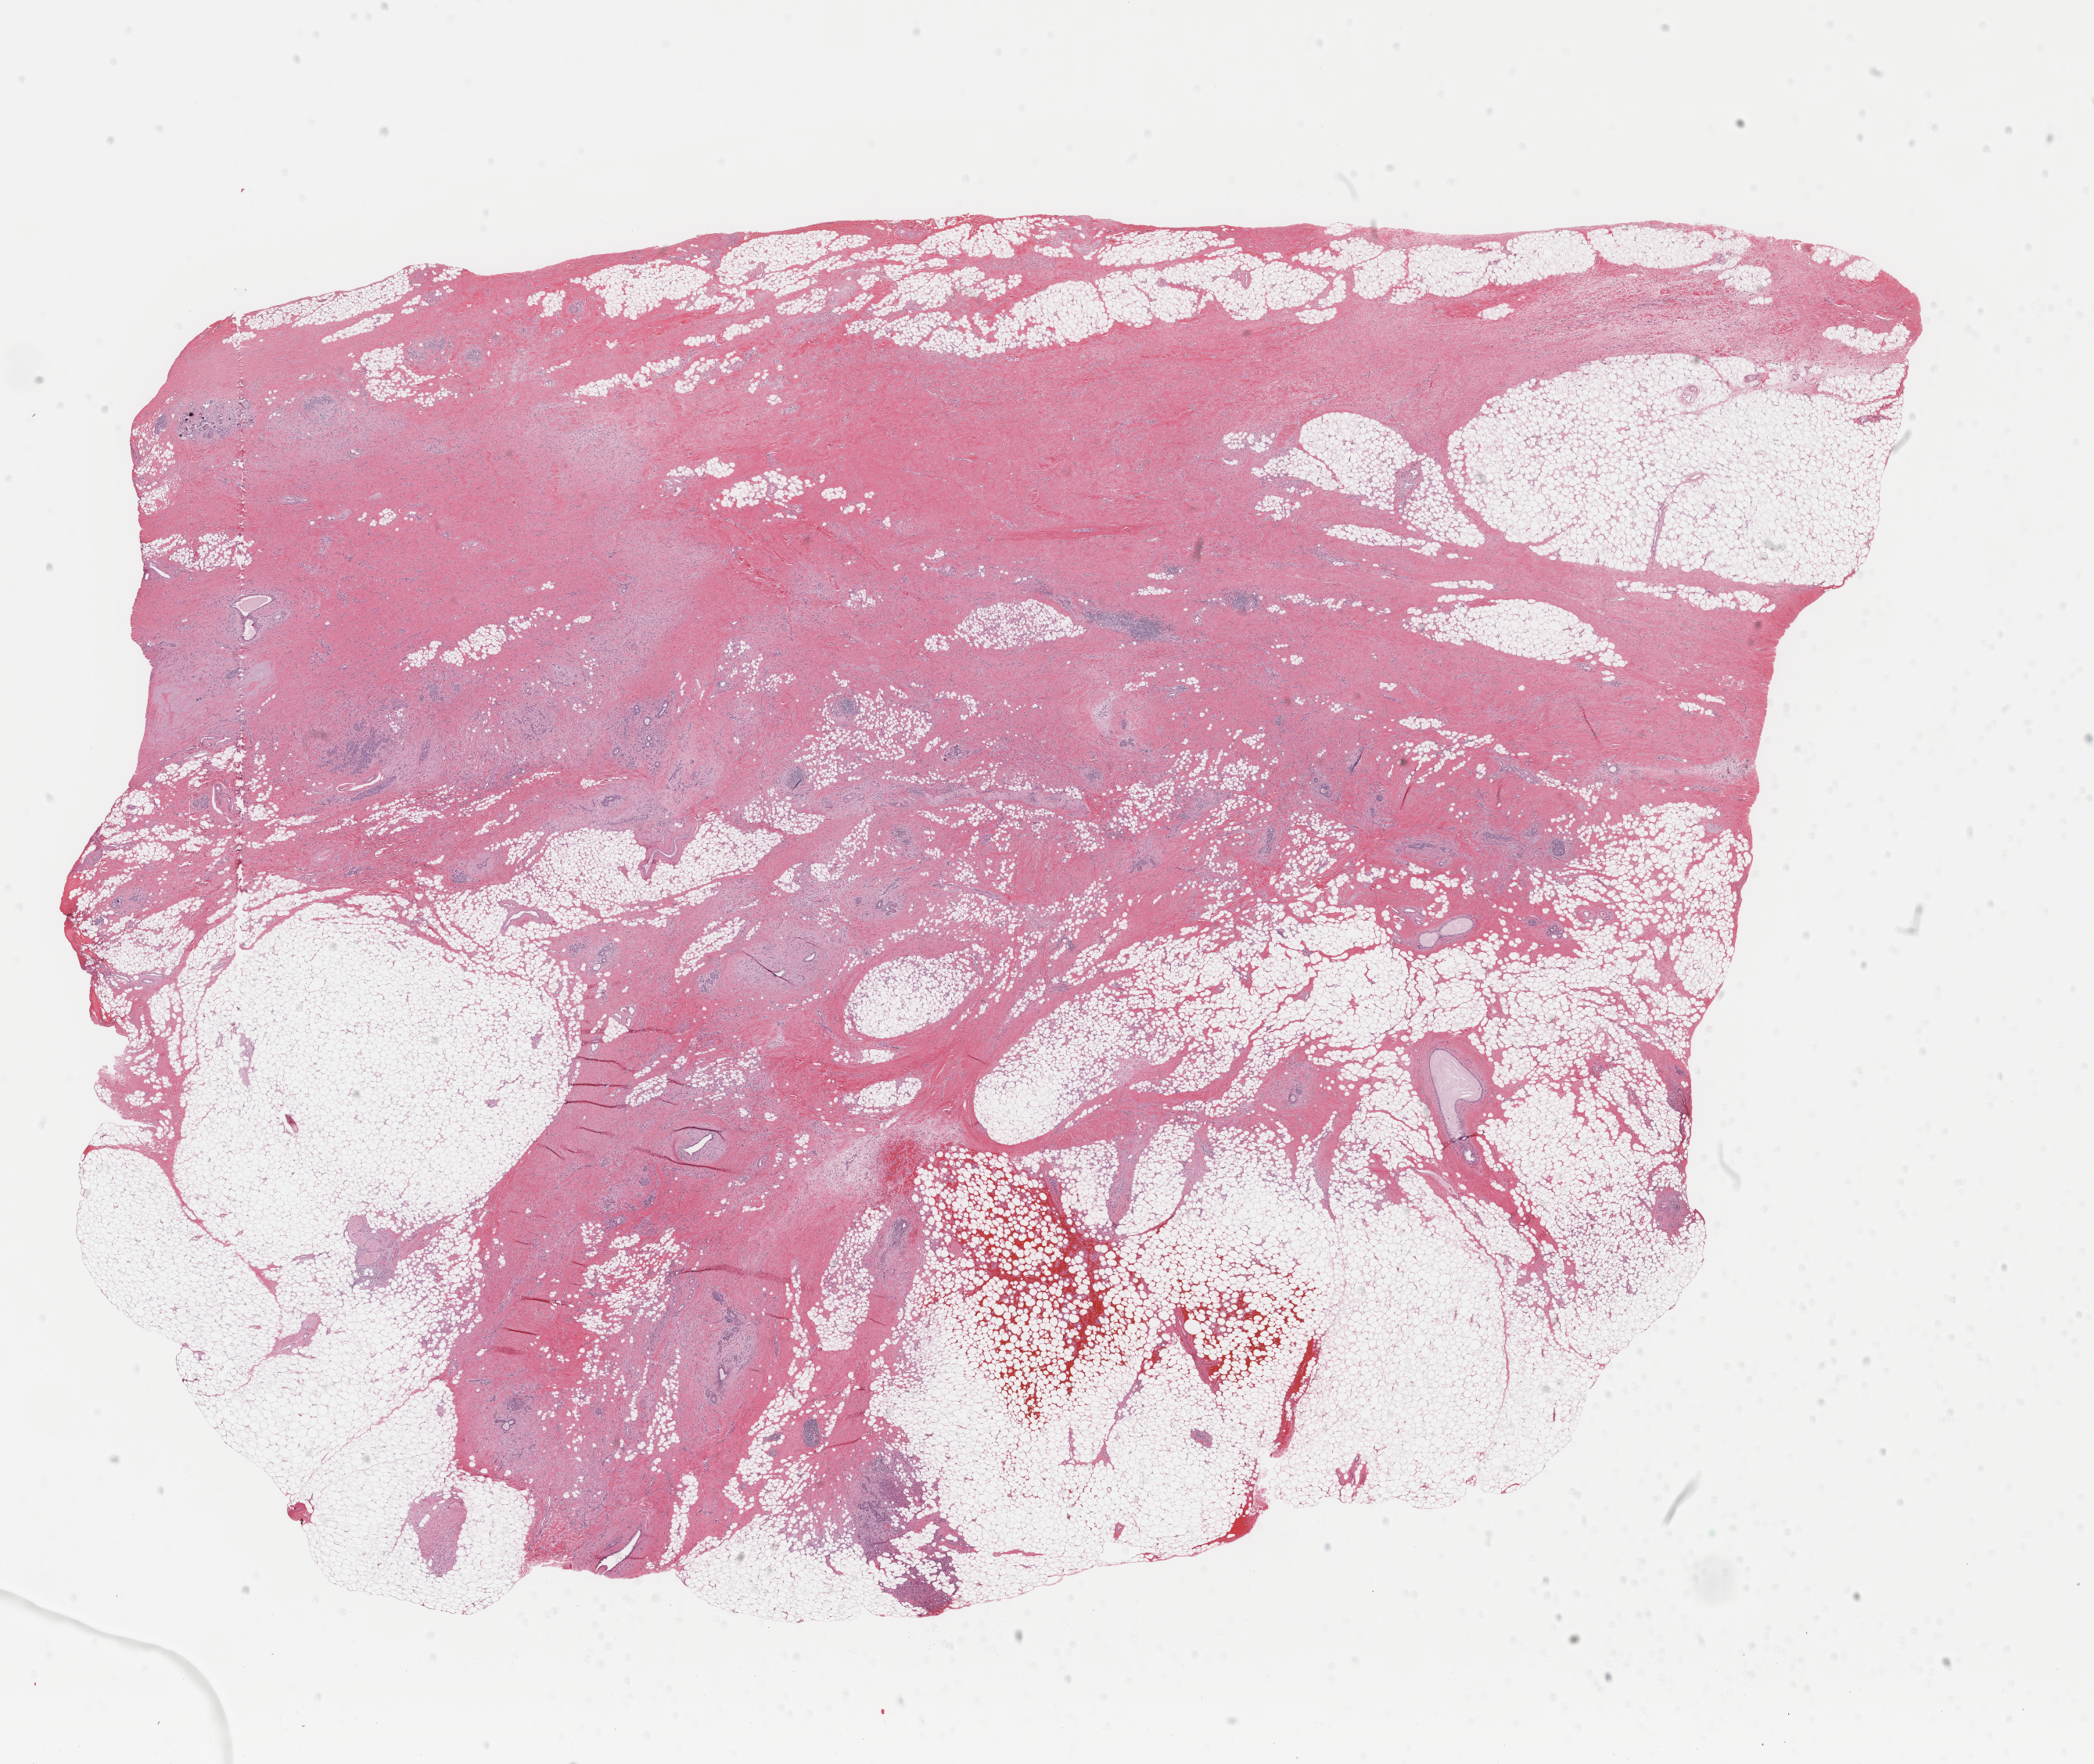
Digitized Hematoxylin and eosin (H&E) stained tissue section (whole slide) — low-resolution overview of the scanned area, about 21.2 x 17.9 mm. Formalin-fixed paraffin-embedded (FFPE) diagnostic section. Sample: primary tumour, breast. Patient: female, age at initial diagnosis 59 years.
• laterality: right
• pathologic diagnosis: Lobular carcinoma, NOS
• AJCC pathologic stage: IIB
• lymph nodes positive (case pathology): 0 of 3 examined